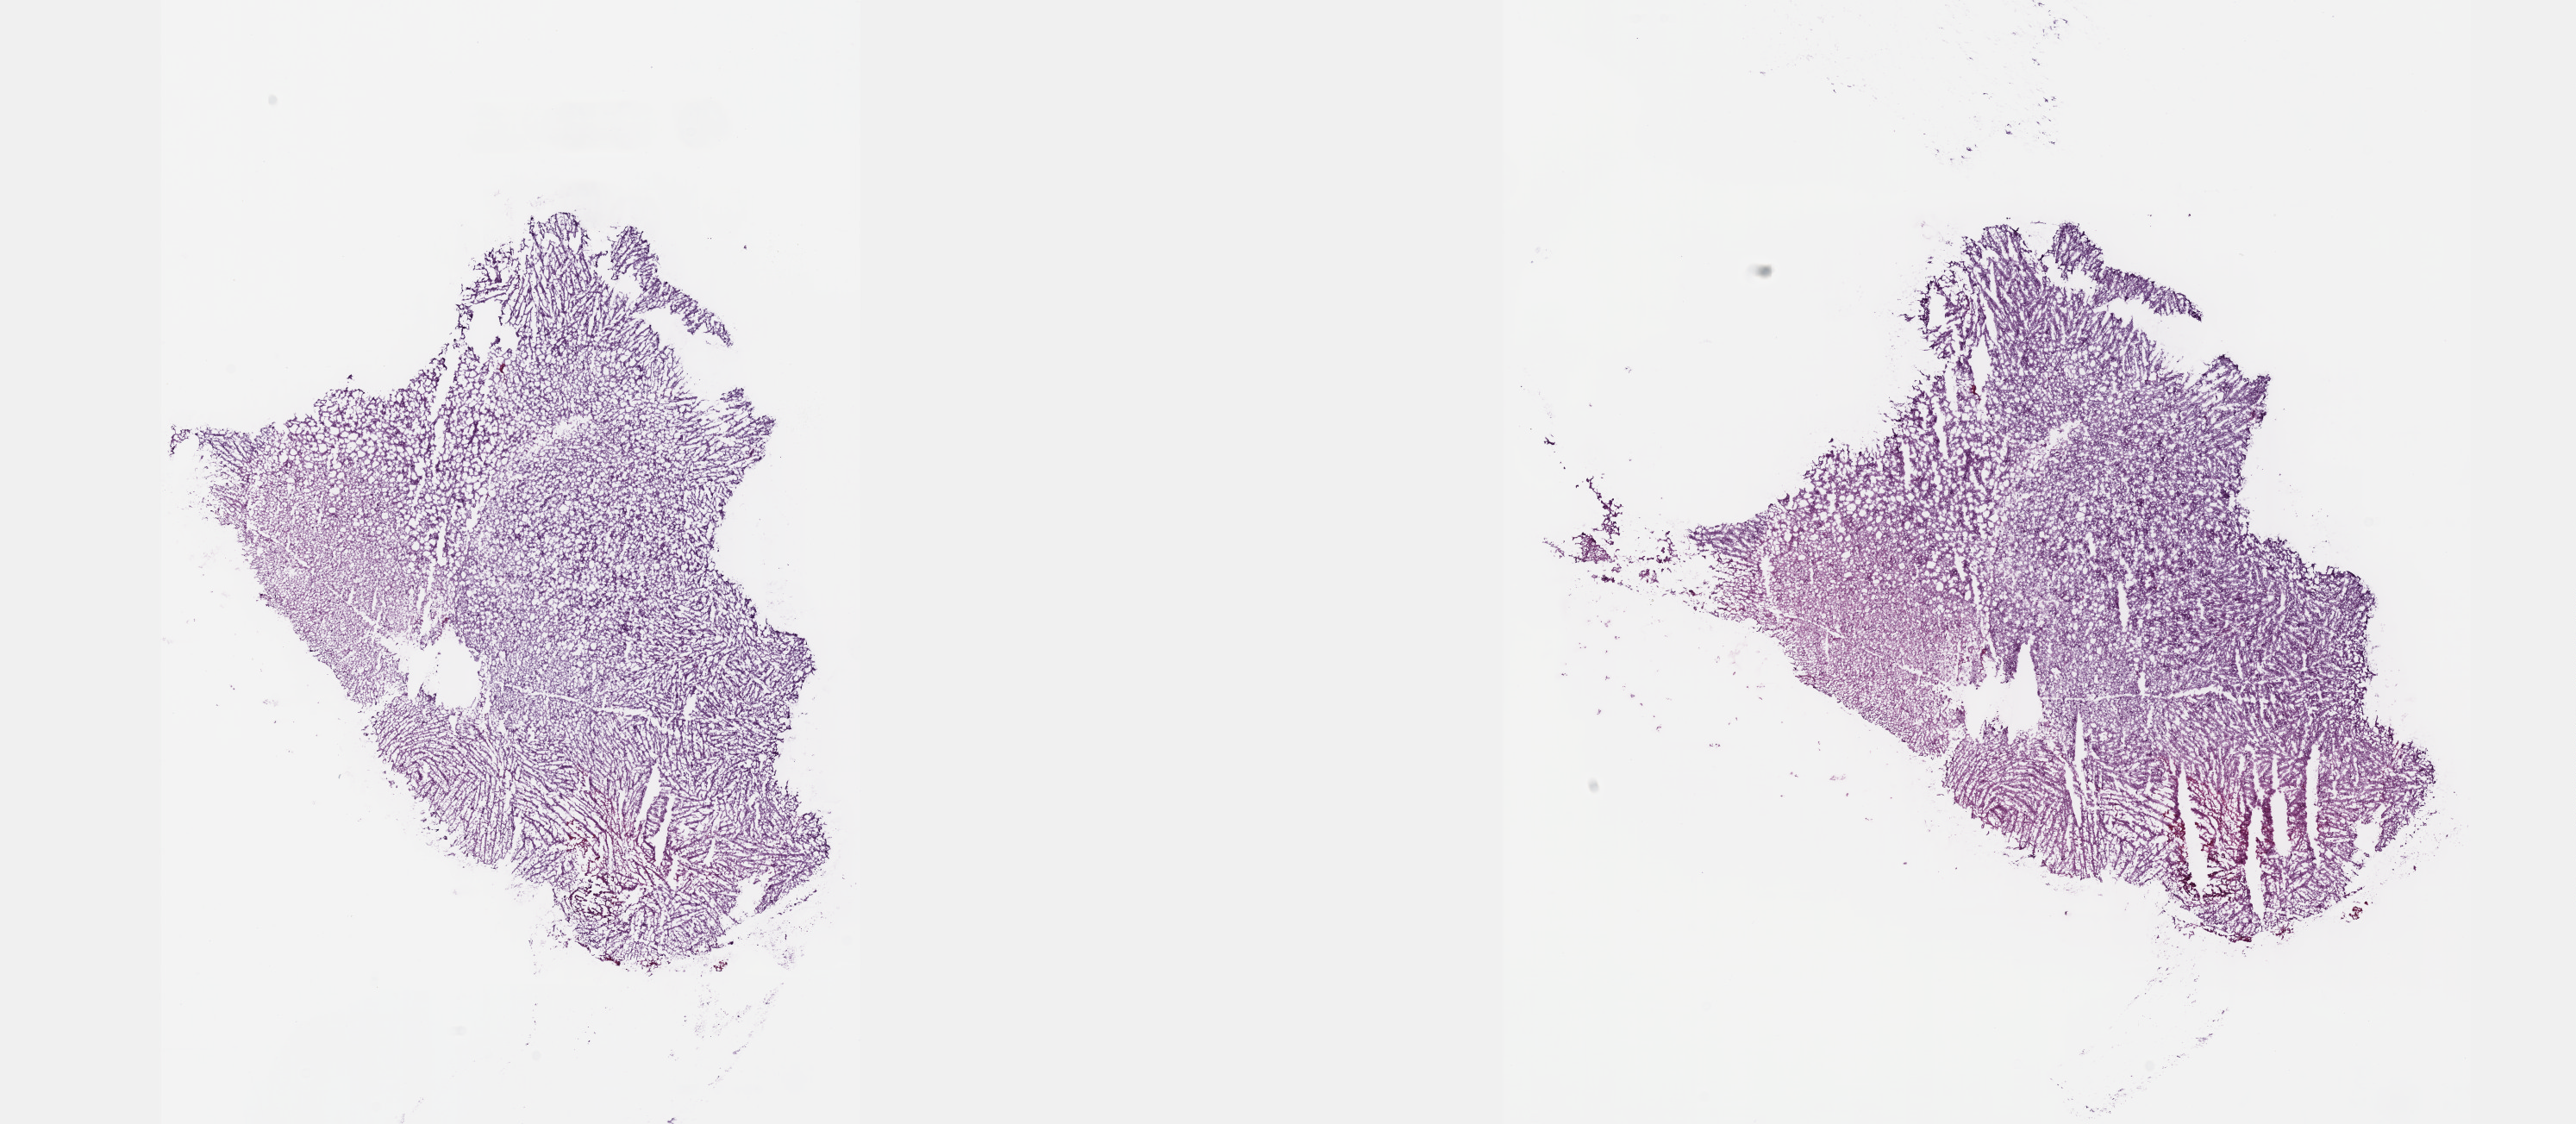
H&E-stained whole-slide image, whole scanned area (about 24.1 x 10.5 mm) shown as a low-resolution overview, frozen section from the top of the tissue portion, sample: primary tumour, brain. Male, age 42 years at initial diagnosis. Histologic grade: G3 (poorly differentiated). Pathologist review of this section (percent, as recorded): tumour cells 40%, tumour nuclei 80%, normal cells 10%, stromal cells 50%, necrosis 0%. Infiltration values recorded for this section: lymphocyte infiltration 0%, monocyte infiltration 0%, neutrophil infiltration 0%.
• histologic diagnosis: Mixed glioma (cerebrum)